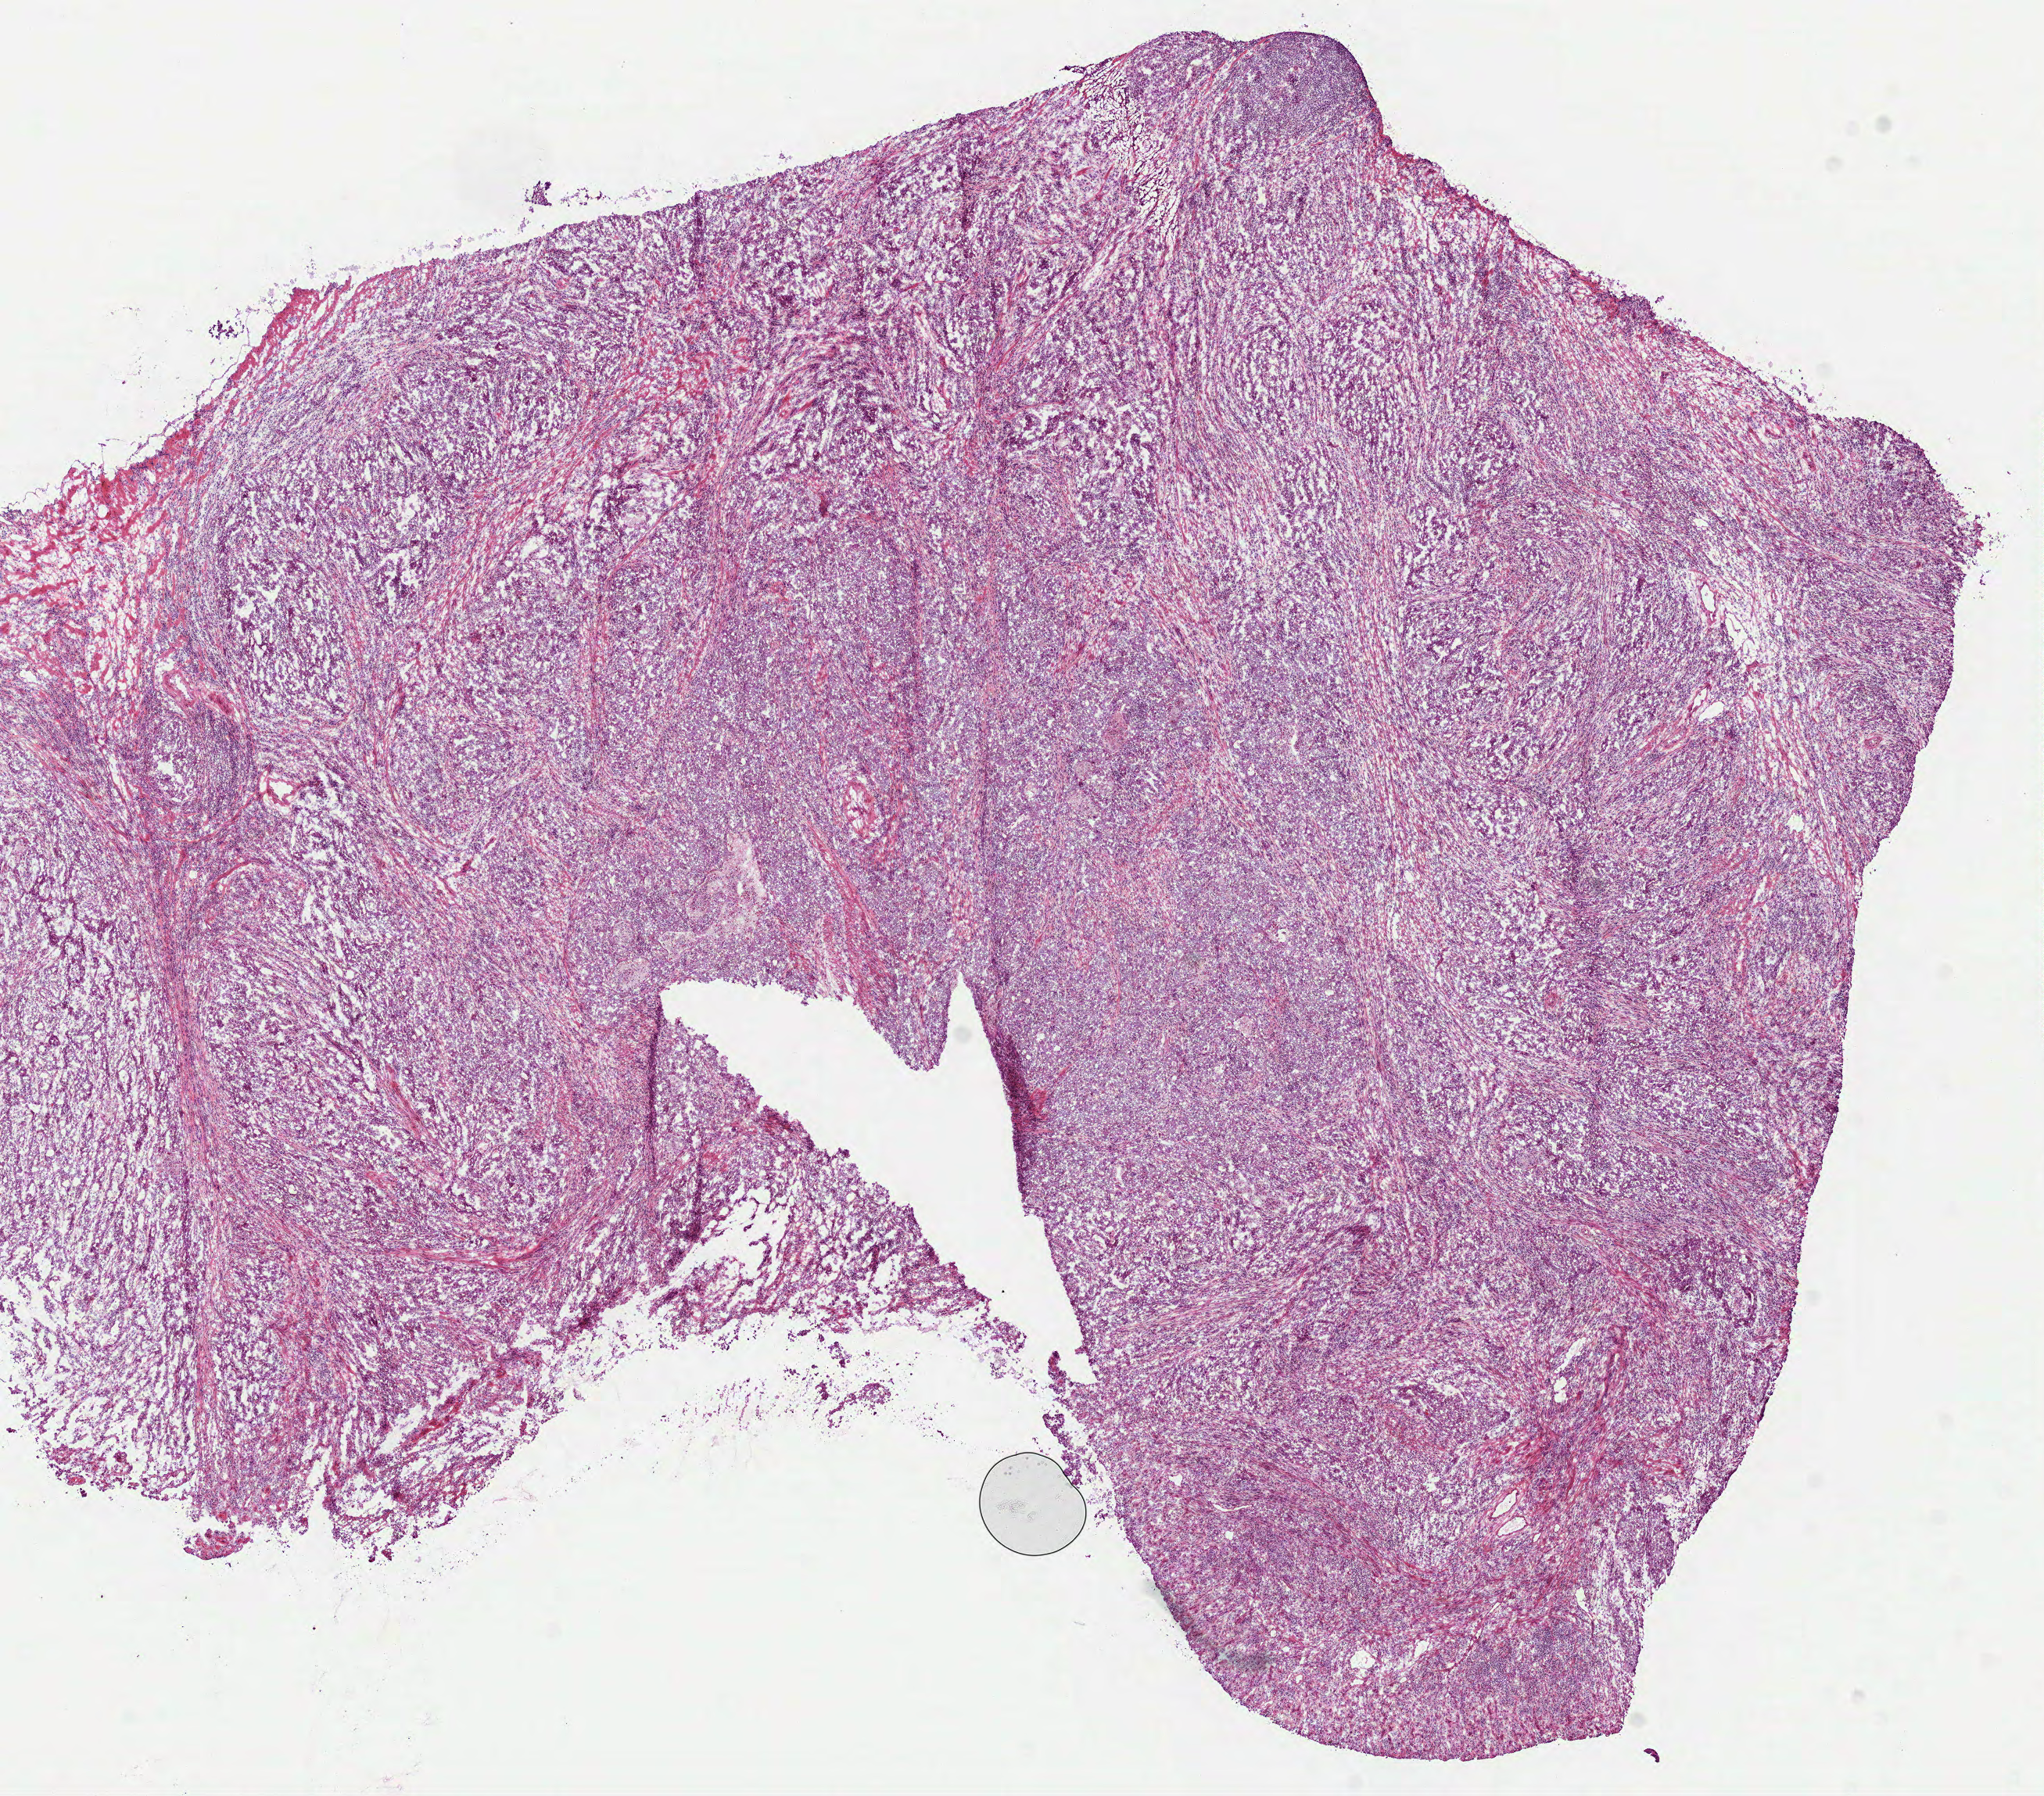
H&E whole-slide image, a low-resolution overview of the entire scanned area, about 10.5 x 9.3 mm (slide scanned at 40x), frozen section from the bottom of the tissue portion, stomach, primary tumour sample. Female, age 73 years at initial diagnosis. Histologic grade: G3 (poorly differentiated). Composition of this section per pathologist review: tumour cells 90%, tumour nuclei 65%, normal cells 0%, stromal cells 10%, necrosis 0%.
Pathologic diagnosis: Adenocarcinoma, intestinal type (fundus of stomach). AJCC pathologic stage: IIIA (6th edition).